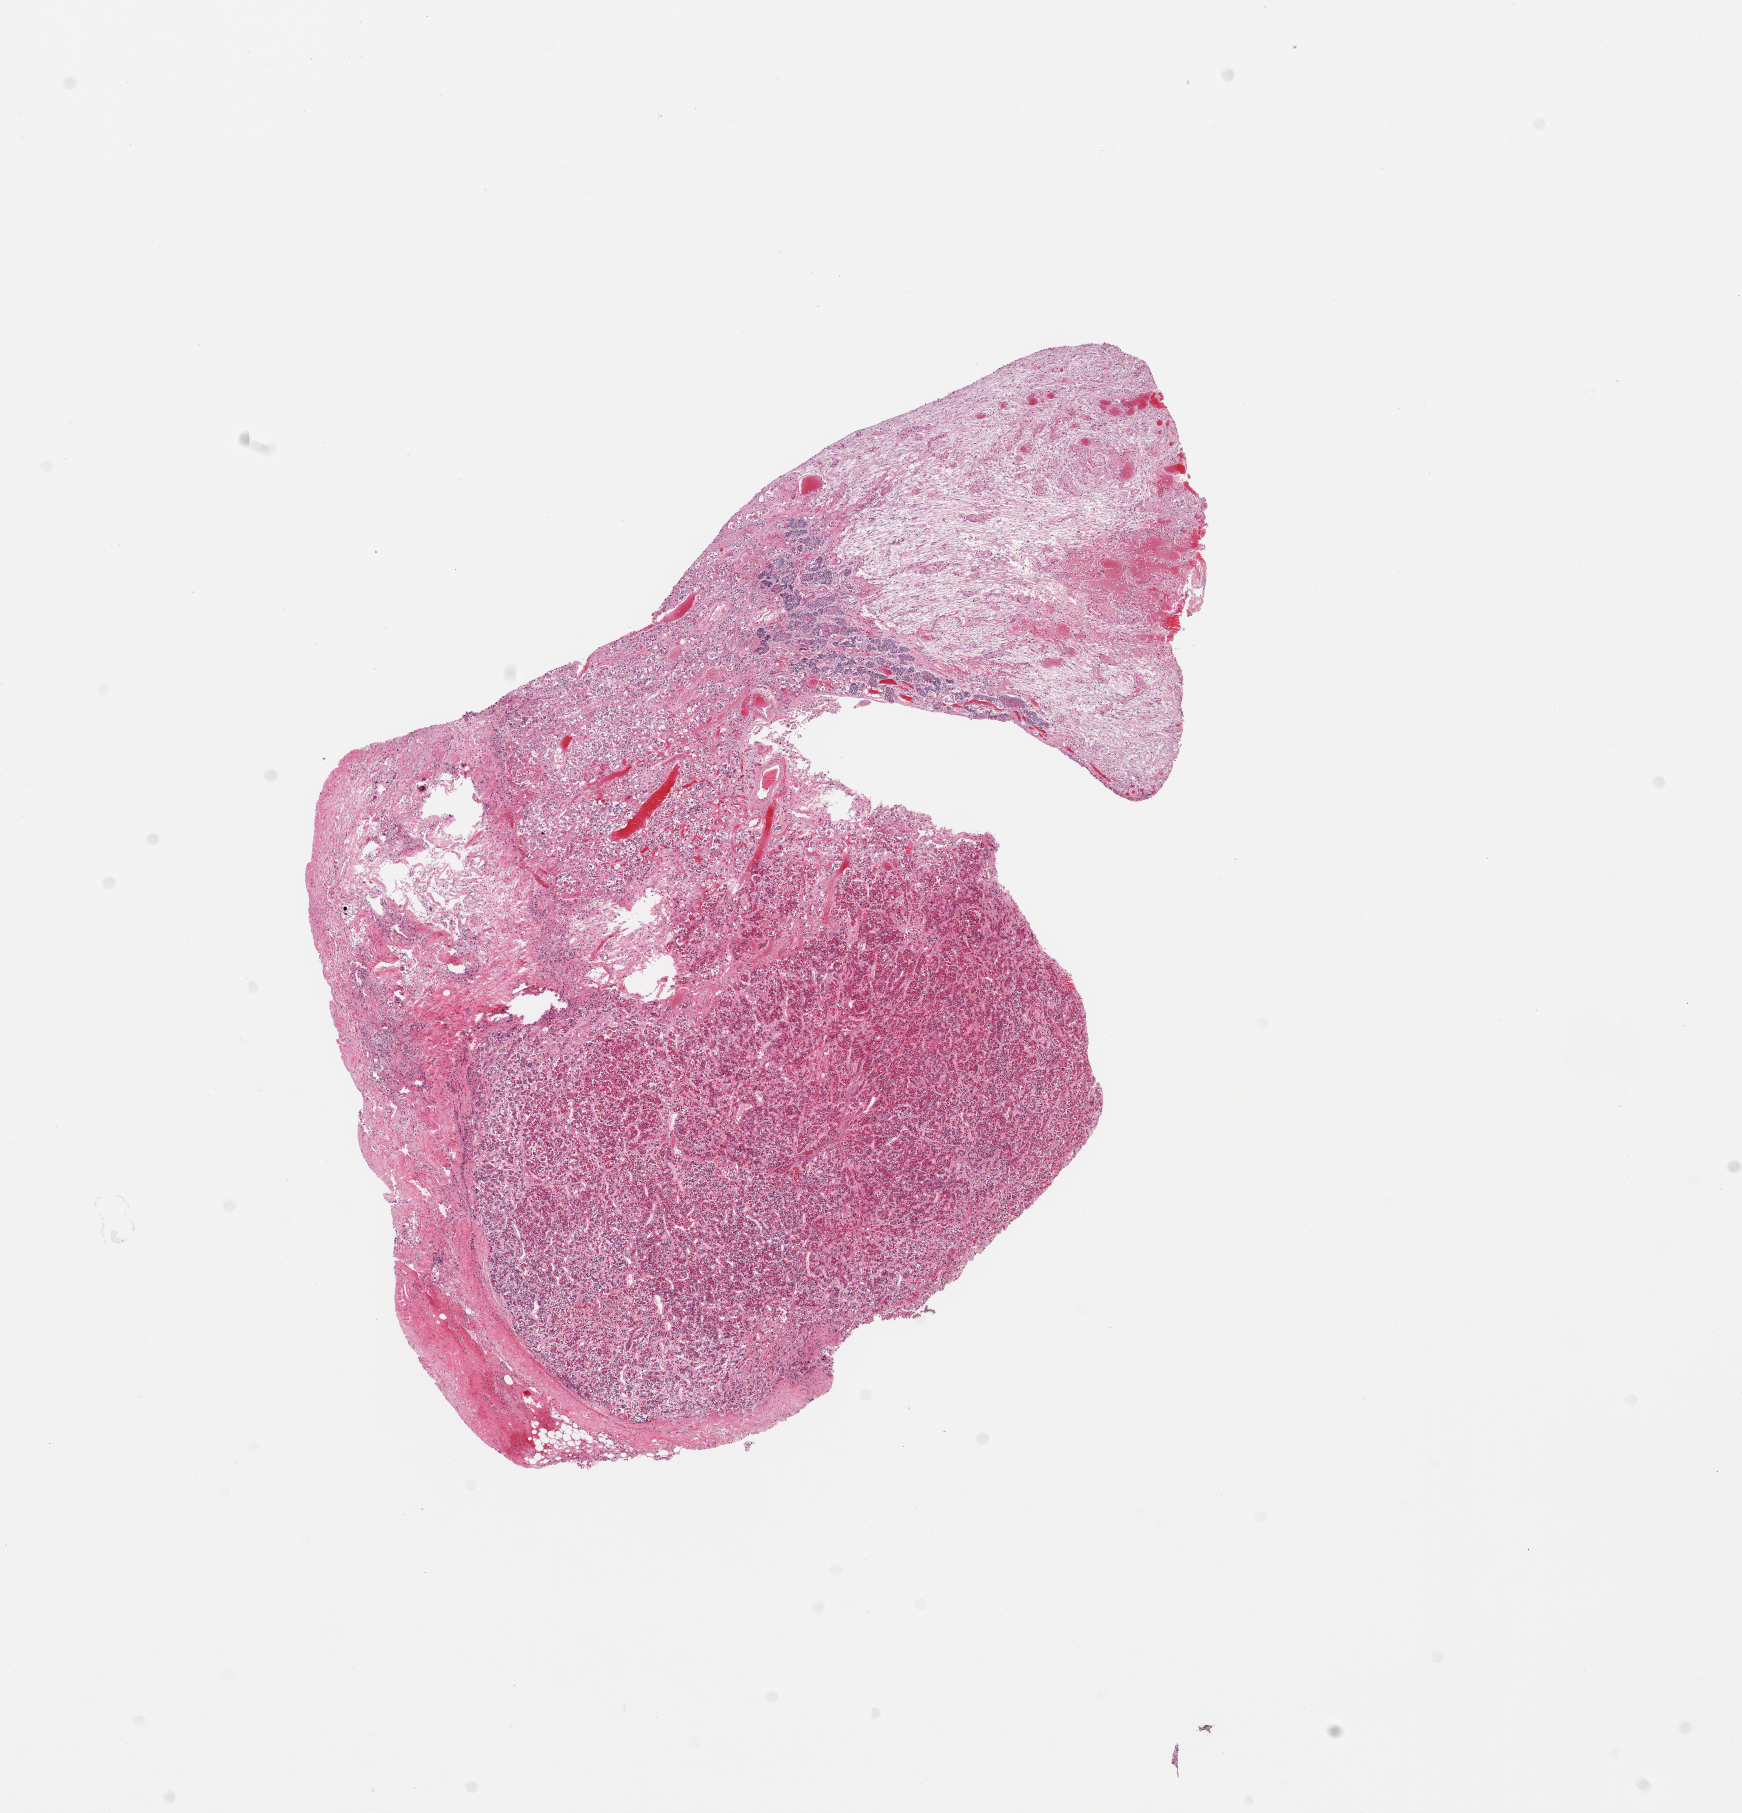
Digitized hematoxylin and eosin (H&E)-stained section, a low-resolution overview of the entire scanned area, about 13.8 x 14.3 mm. PAXgene-fixed paraffin-embedded (PFPE) section. Section of pituitary (target tissue). Tissue donor sample. Donor sex: female.
Reviewer comment on this tissue sample: 1 piece; adenohypophysis and neurohypophysis with some squamous nests.